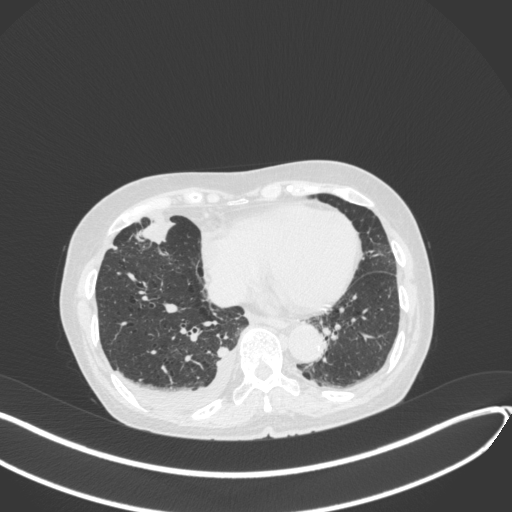
Chest CT, one axial slice. 120 kVp. Lung window (W 1500 / L -600 HU). 512 × 512 image matrix, field of view 400 × 400 mm. Patient: female, 75 years. From the clinical record (not read from this slice): clinical TNM (as recorded): T2a N3 M0.
Annotated regions visible in this slice (rectangle marked by the reading radiologist):
- lung tumour (recorded histology: adenocarcinoma): box from (x=133, y=215) to (x=180, y=248) px